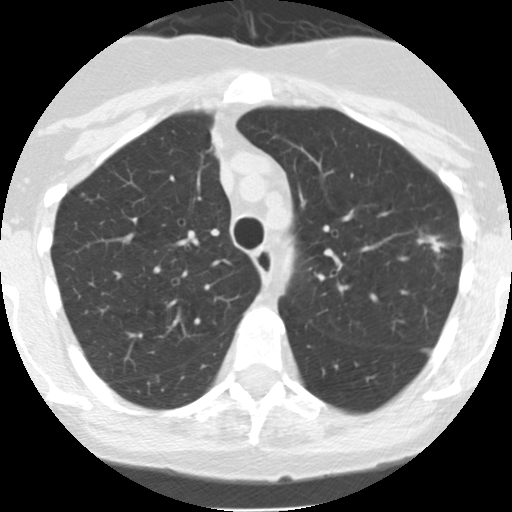
Low-dose screening chest CT, one axial slice; lung window (W 1500 / L -600 HU); 512 × 512 image matrix.
Outlined on this slice (expert manual segmentation):
- lesion 1 (tumor, upper lobe of left lung): bounding box [x1, y1, x2, y2] px = [417, 235, 445, 253]